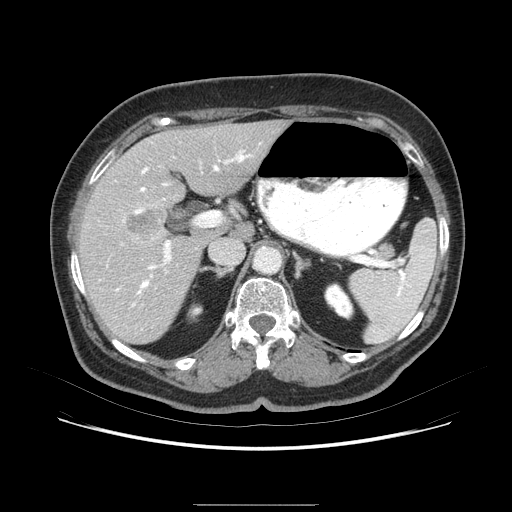
Contrast-enhanced abdominal CT (liver protocol), one axial slice; position 46 of 79 along the scan axis; 120 kVp; soft-tissue window (W 400 / L 40 HU); 2.5 mm slice thickness; 512 × 512 image matrix. Case-level facts recorded for this patient, not image findings: diagnosis: hepatocellular carcinoma (patient treated with transarterial chemoembolisation; whether this scan precedes or follows treatment is not stated here); TNM stage (as recorded): Stage-I; Child-Pugh class: A; tumour differentiation: poorly differentiated; tumour nodularity: uninodular.
Annotated regions visible in this slice (semi-automatically segmented with operator editing):
- liver parenchyma outside the tumour (the mass and vessels are separate outlines, so this box may not span the whole liver): bounding box <76,122,294,346> (left, top, right, bottom; pixels)
- mass: <129,197,171,237>
- liver vessels: <110,154,250,319>